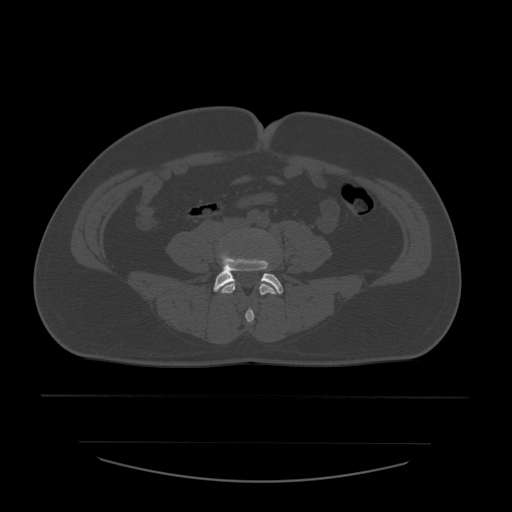
CT including the spine, one axial slice; position 132 of 532 along the scan axis; reconstruction kernel STANDARD; 120 kVp; bone window (W 1800 / L 400 HU); 512 × 512 image matrix, field of view 441 × 441 mm. Patient age 44 years. From the clinical record (not read from this slice): primary cancer: soft tissue sarcoma.
Outlined on this slice (semi-automatic segmentation, software-assisted and operator-edited):
- L4 vertebra: bounding box <221,234,279,323> (left, top, right, bottom; pixels)
- L5 vertebra: <213,254,283,294>